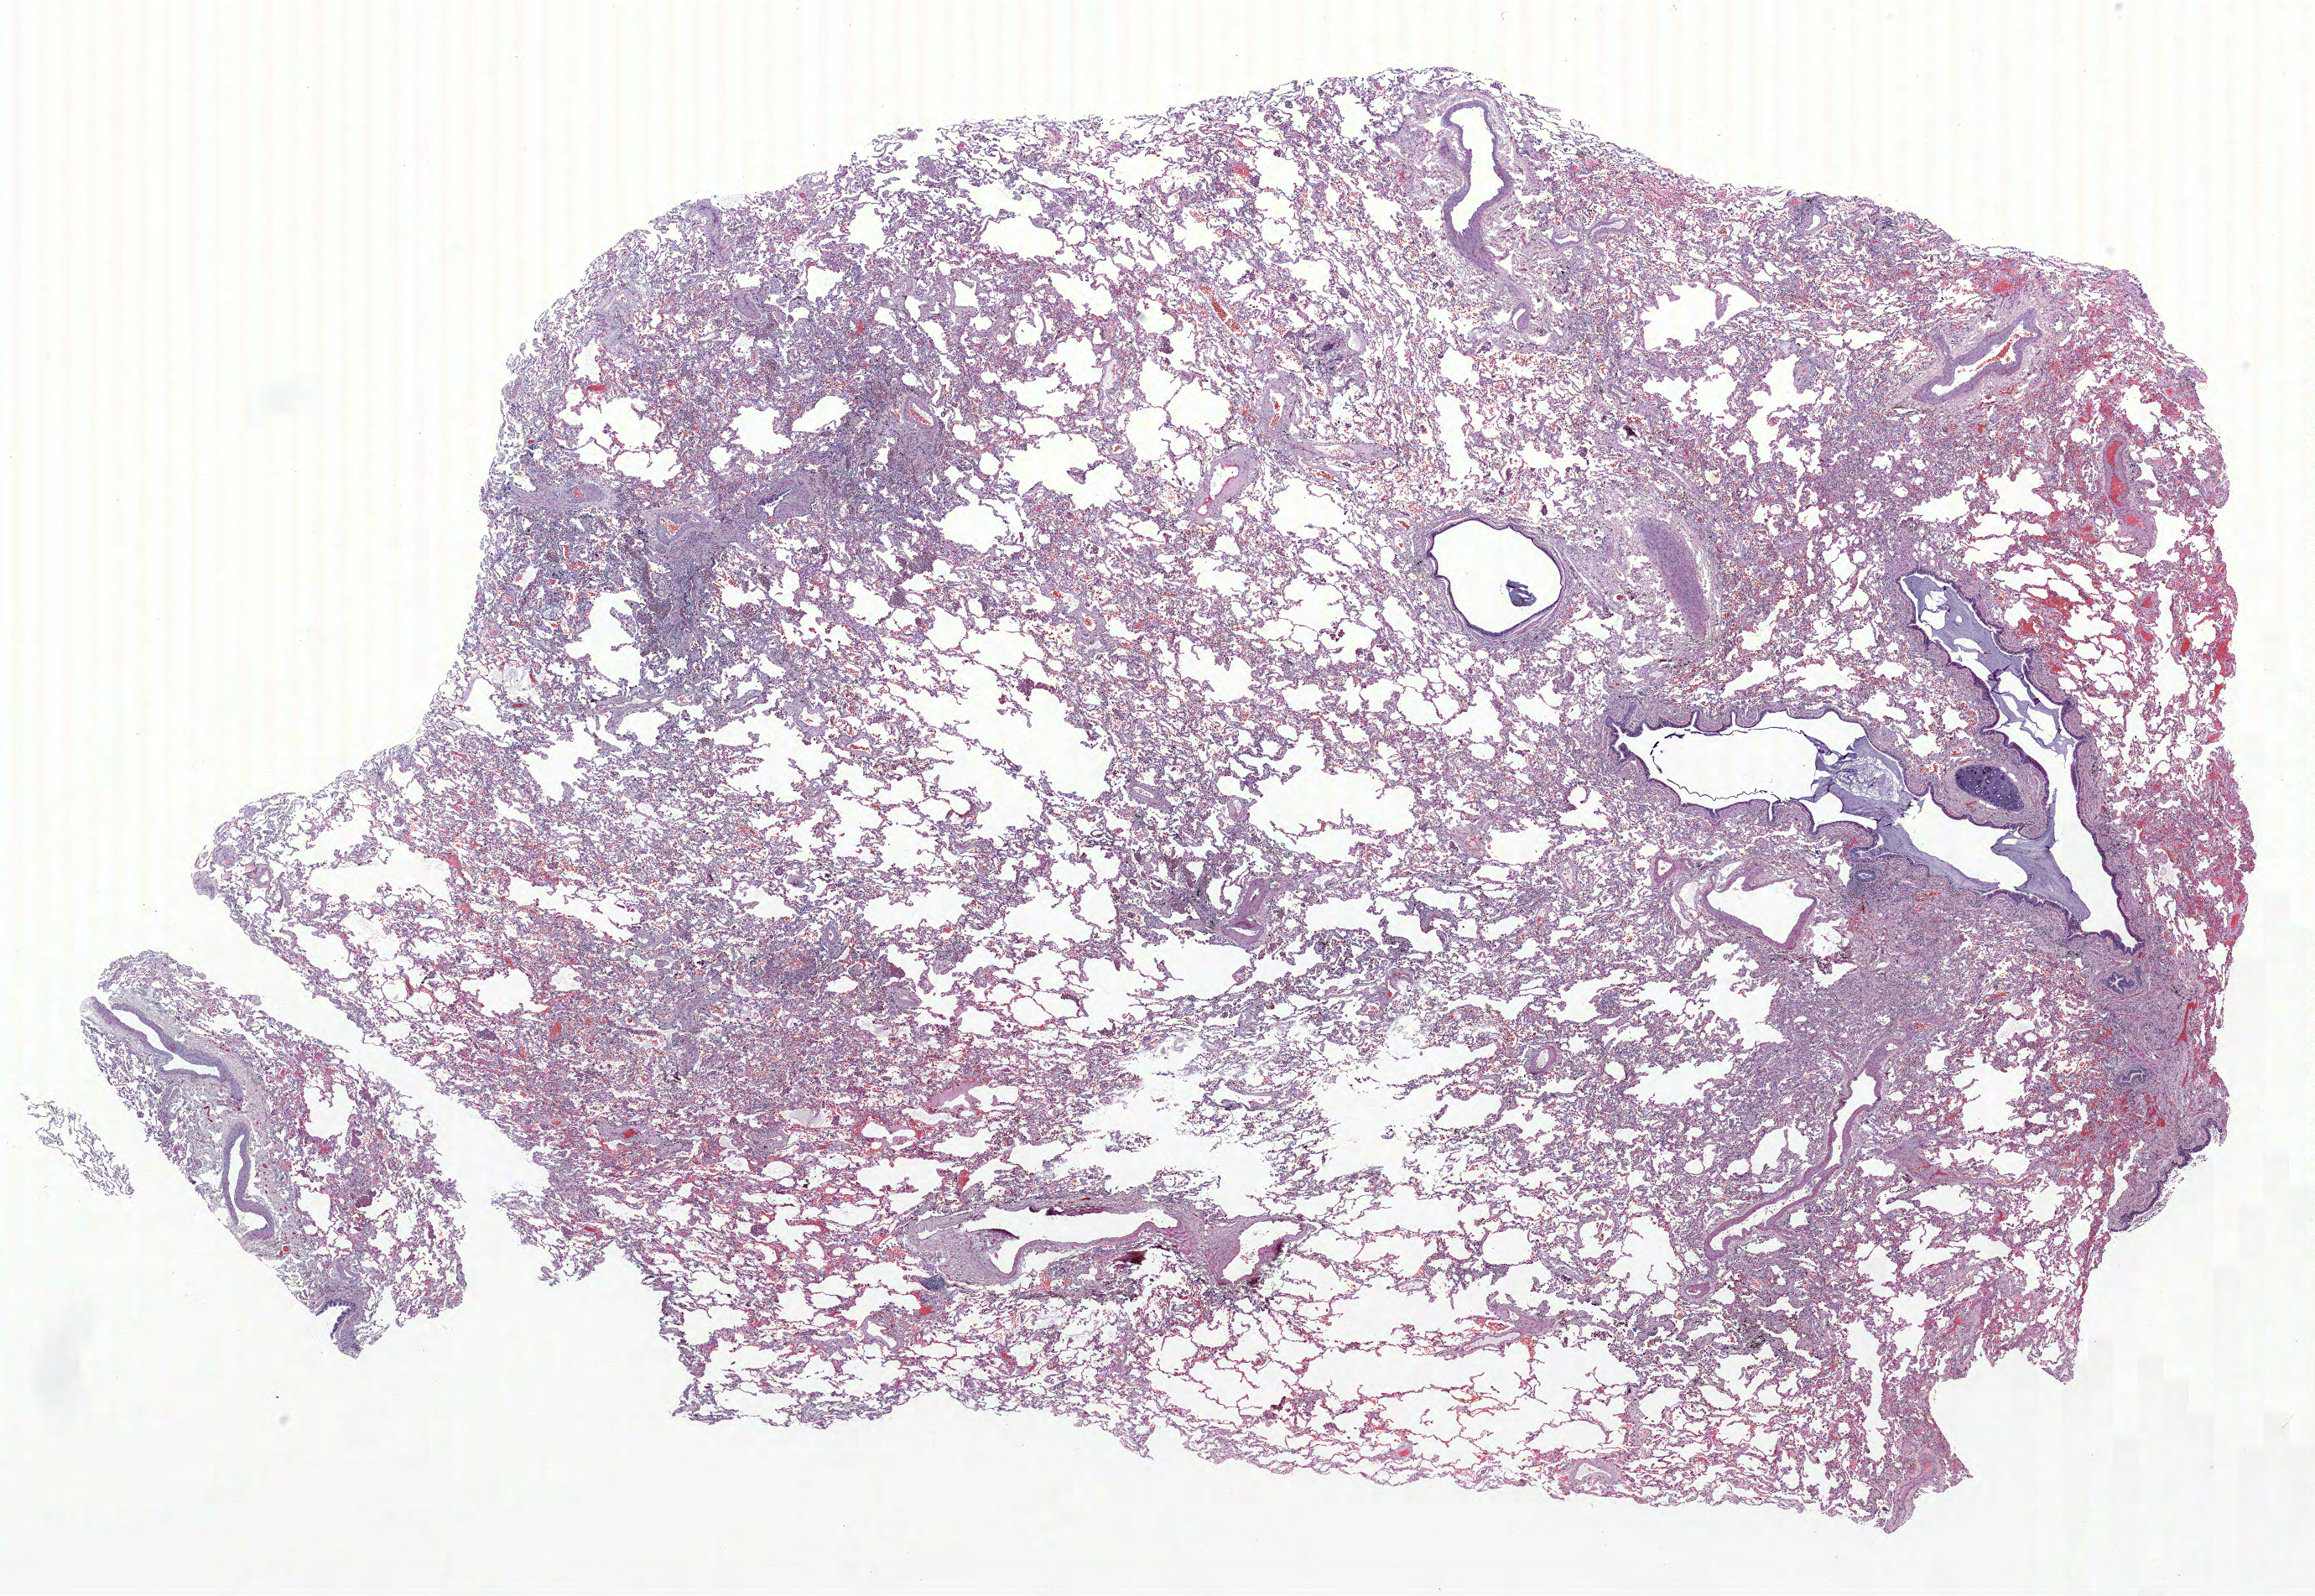
Whole-slide histology image, H&E, low-resolution overview of the scanned area, about 22.1 x 15.2 mm (from a 40x scan). Formalin-fixed paraffin-embedded (FFPE) section. Lung tissue. Female, age 57 at enrolment. Current smoker at enrolment. Grade: well differentiated (G1).
Tumour size (pathology): 16 mm. Participant's lung-cancer diagnosis: Bronchiolo-alveolar adenocarcinoma, NOS (ICD-O-3 8250/3). ICD-O-3 topography: lower lobe of lung (C34.3). Primary tumour location (clinical record): left lower lobe. Stage (AJCC 6th edition): IA.